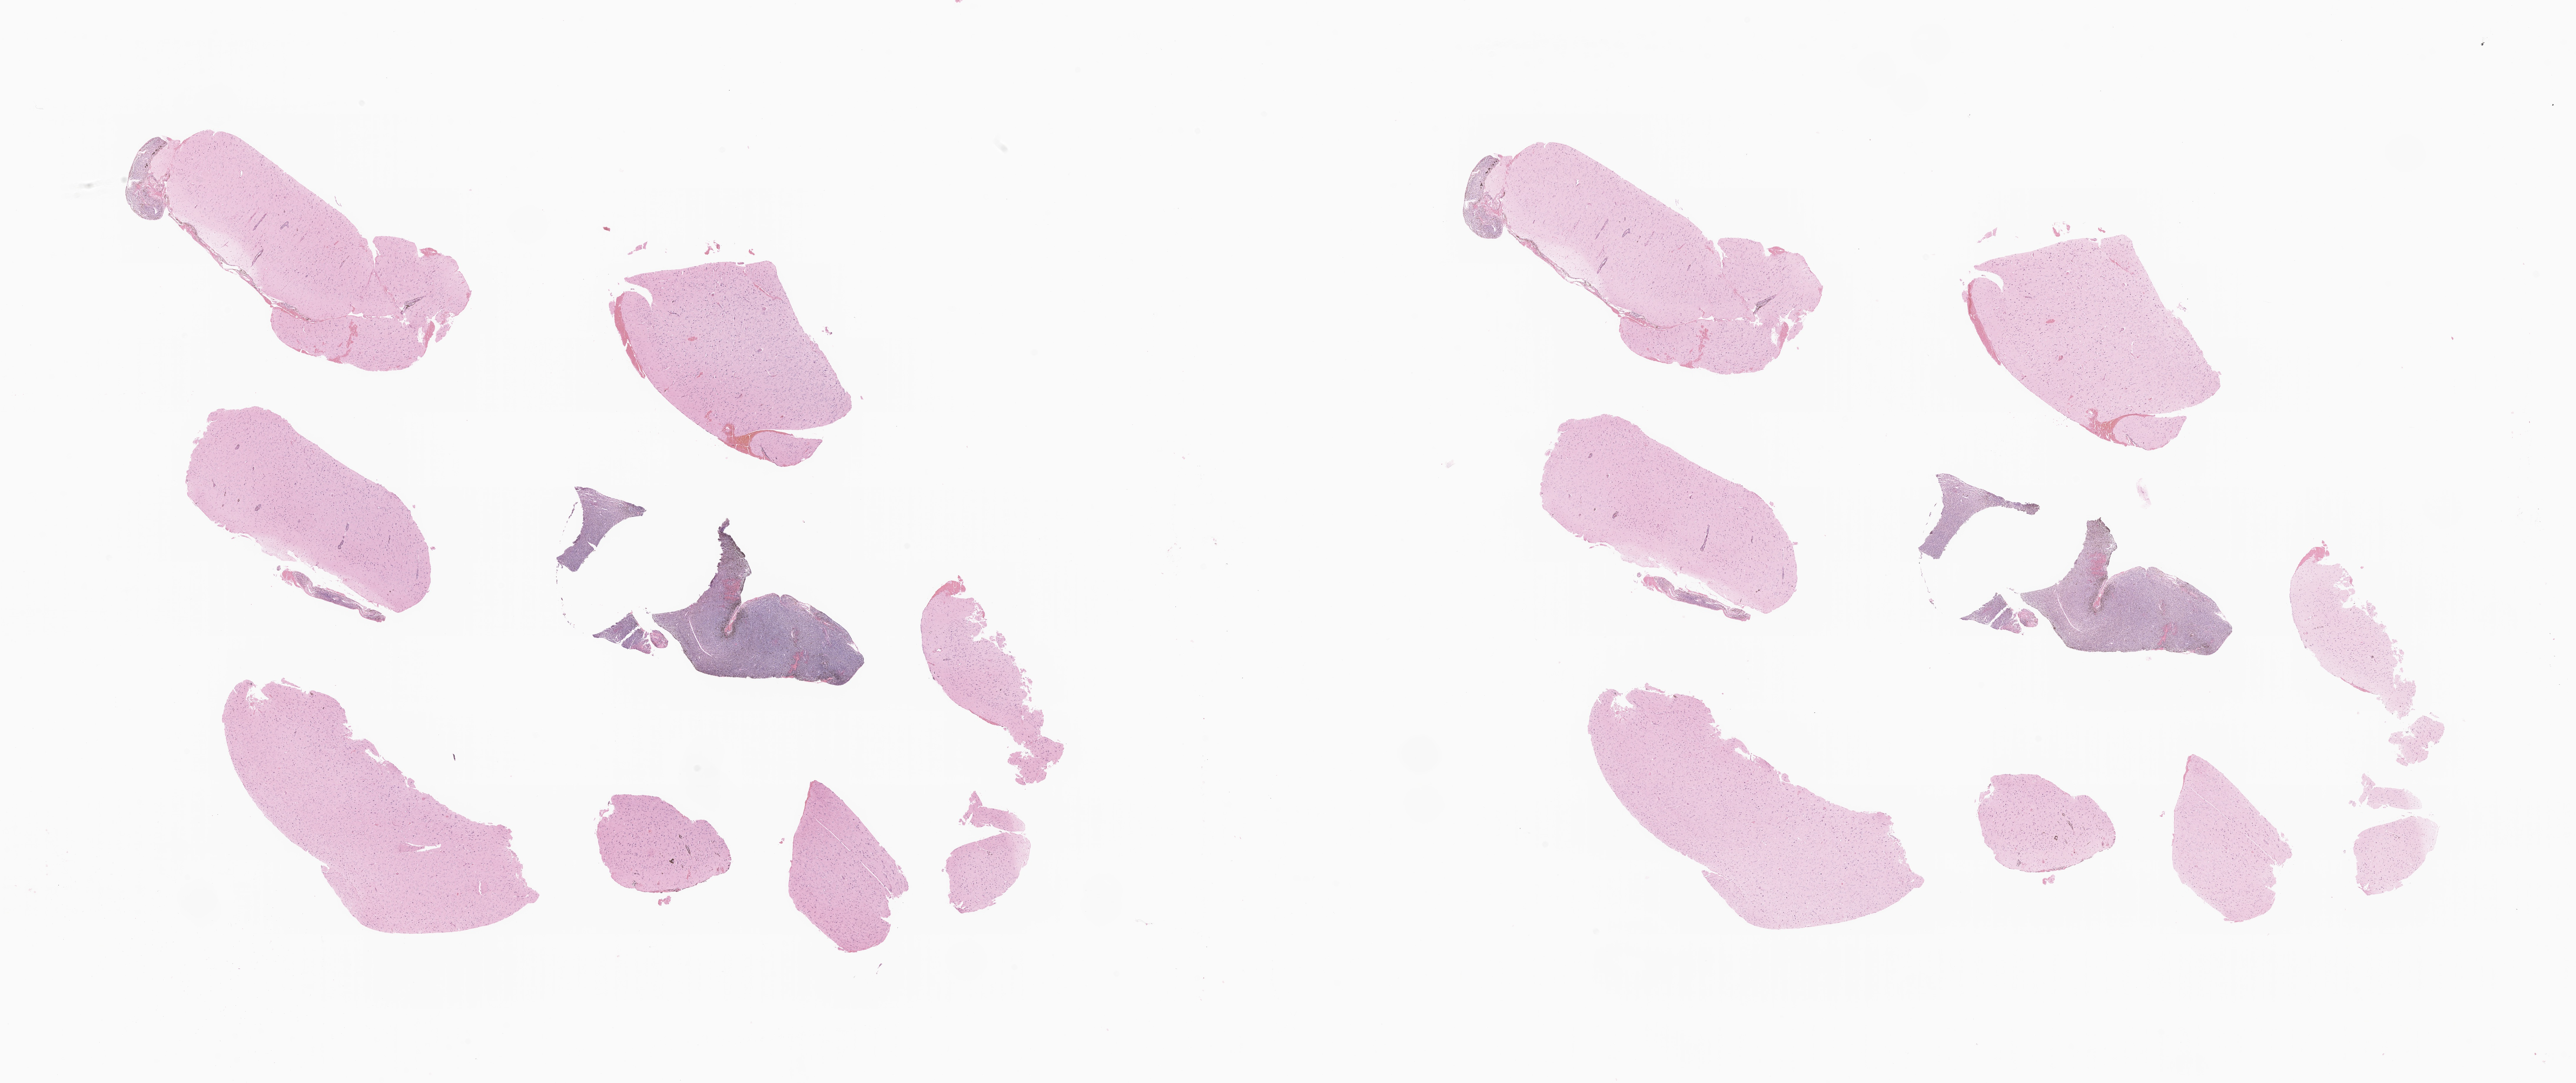
Digitized H&E-stained section of tumor tissue from the brain — low-resolution overview of the scanned area, about 36.9 x 15.5 mm; FFPE section. Patient male; age 148 months (12 years 4 months).
Recorded diagnosis: Malignant melanoma, NOS.